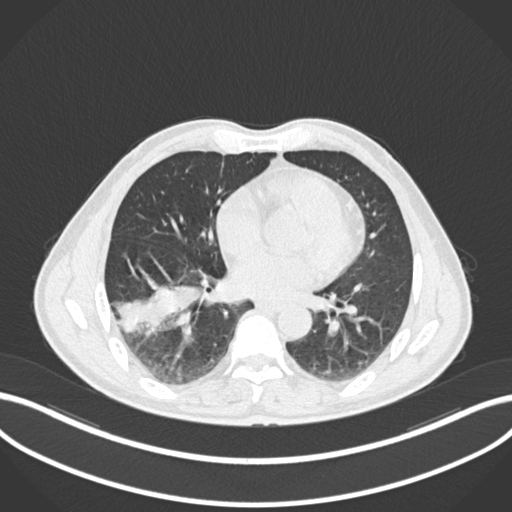
Chest CT, one axial slice. Slice 80 of 208 in the series (ordered by position). 120 kVp. Lung window (W 1500 / L -600 HU). 1 mm slice thickness. 512 × 512 image matrix, field of view 400 × 400 mm. Patient: male, 58 years. Case-level facts recorded for this patient, not image findings: clinical TNM (as recorded): T3 N0 M0; histopathological grade: G2.
Outlined on this slice (bounding box drawn by a radiologist):
- lung tumour (recorded histology: squamous cell carcinoma): bounding box [x1, y1, x2, y2] px = [115, 274, 200, 343]